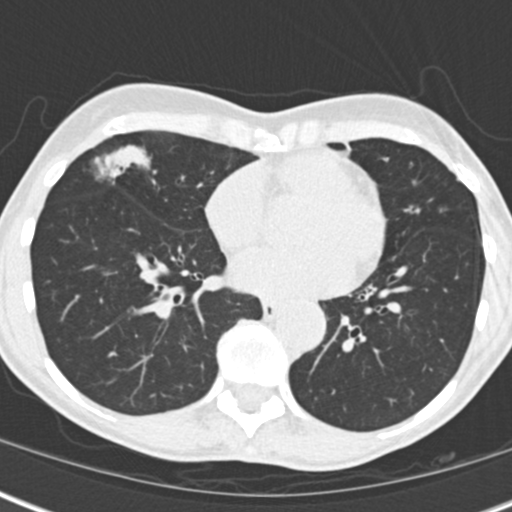
Low-dose screening chest CT, one axial slice; position 69 of 173 along the scan axis; 120 kVp; lung window (W 1500 / L -600 HU); 2 mm slice thickness; 512 × 512 image matrix, field of view 290 × 290 mm.
Outlined on this slice (expert manual segmentation):
- lesion 1 (tumor, middle lobe of right lung): bounding box <104,146,149,178> (left, top, right, bottom; pixels)